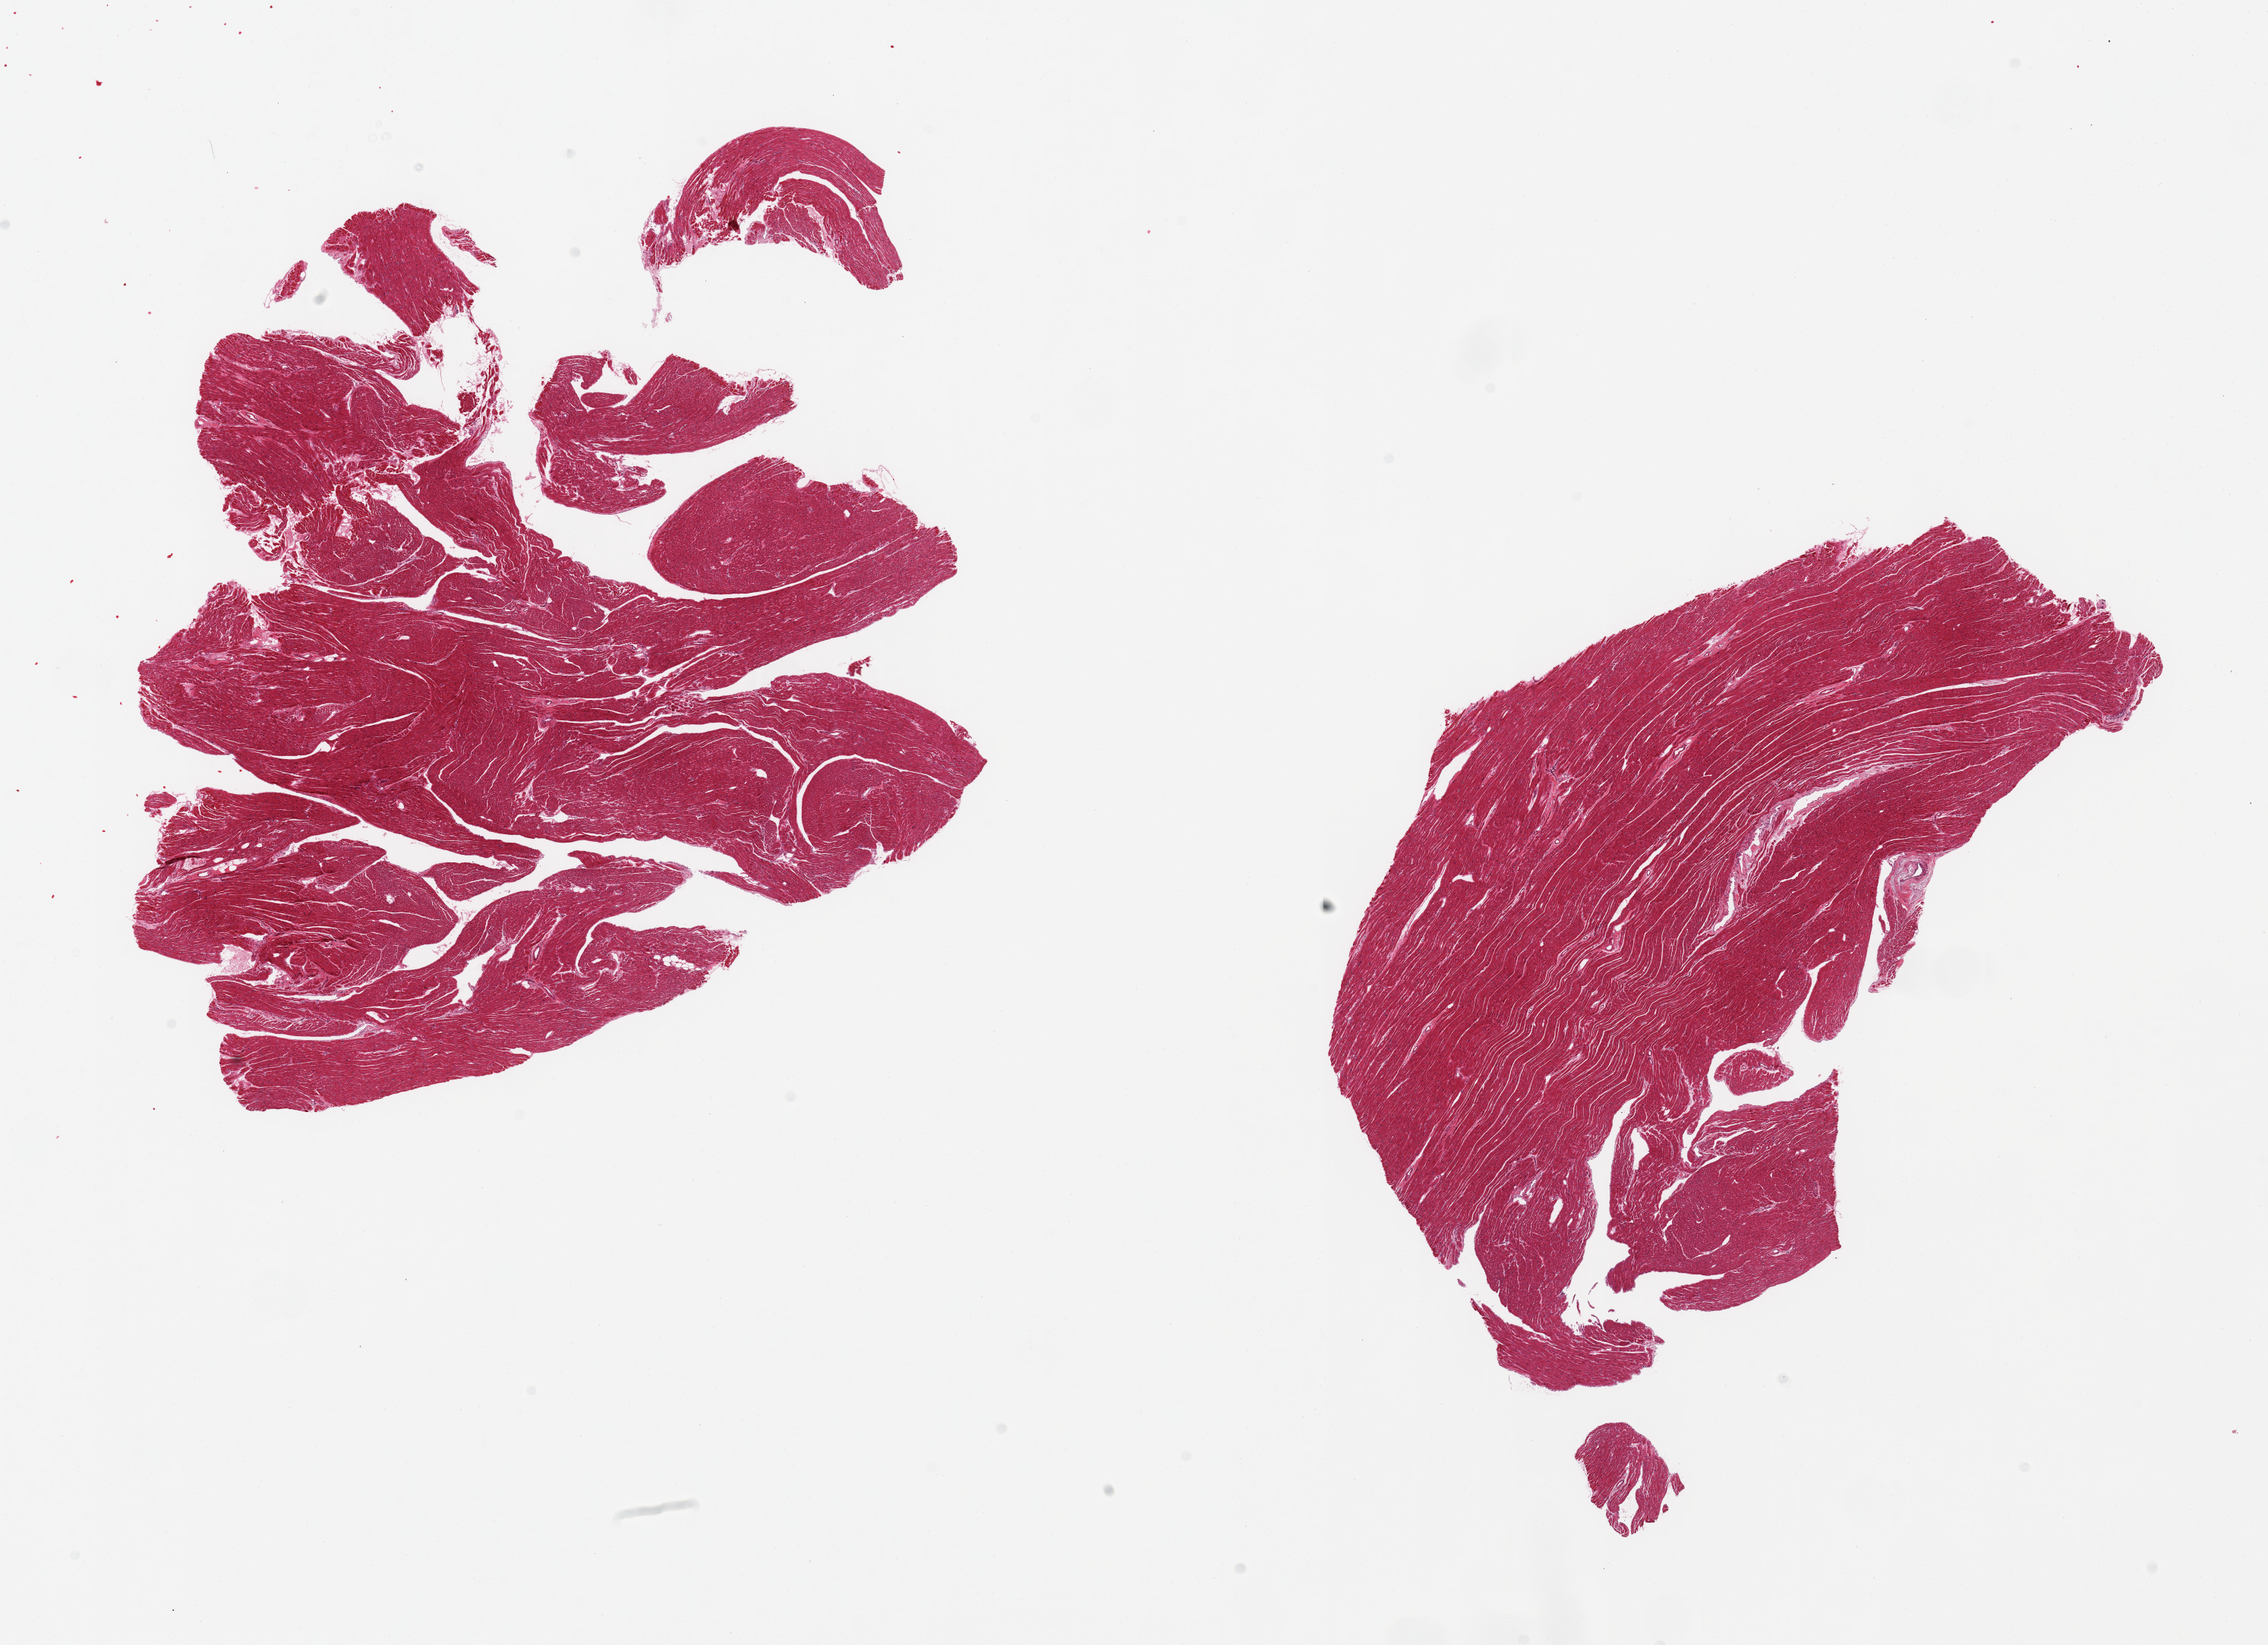
Whole-slide image, H&E stain, low-resolution overview of the scanned area, about 23.6 x 17.1 mm, PAXgene-fixed, paraffin-embedded tissue, sampled site (target tissue): heart, tissue donor sample. Donor: female.
* review note (as recorded): 2 pieces